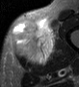
MRI of an extremity soft-tissue mass, one axial slice. Slice 16 of 45 in the series (ordered by position). STIR. MR volume resampled by the dataset authors to the PET/CT grid (not the native acquisition matrix). 3.27 mm slice thickness. 79 × 87 image matrix, field of view 77 × 85 mm. Male patient. Case-level facts recorded for this patient, not image findings: histological type: pleiomorphic leiomyosarcoma; grade: high; site of the primary tumour: left thigh.
Outlined on this slice (expert contour drawn on MRI and transferred to this co-registered scan by the dataset authors):
- gross tumour volume including surrounding oedema: bounding box [x1, y1, x2, y2] px = [11, 18, 58, 65]
- gross tumour volume (mass): [11, 20, 55, 65]